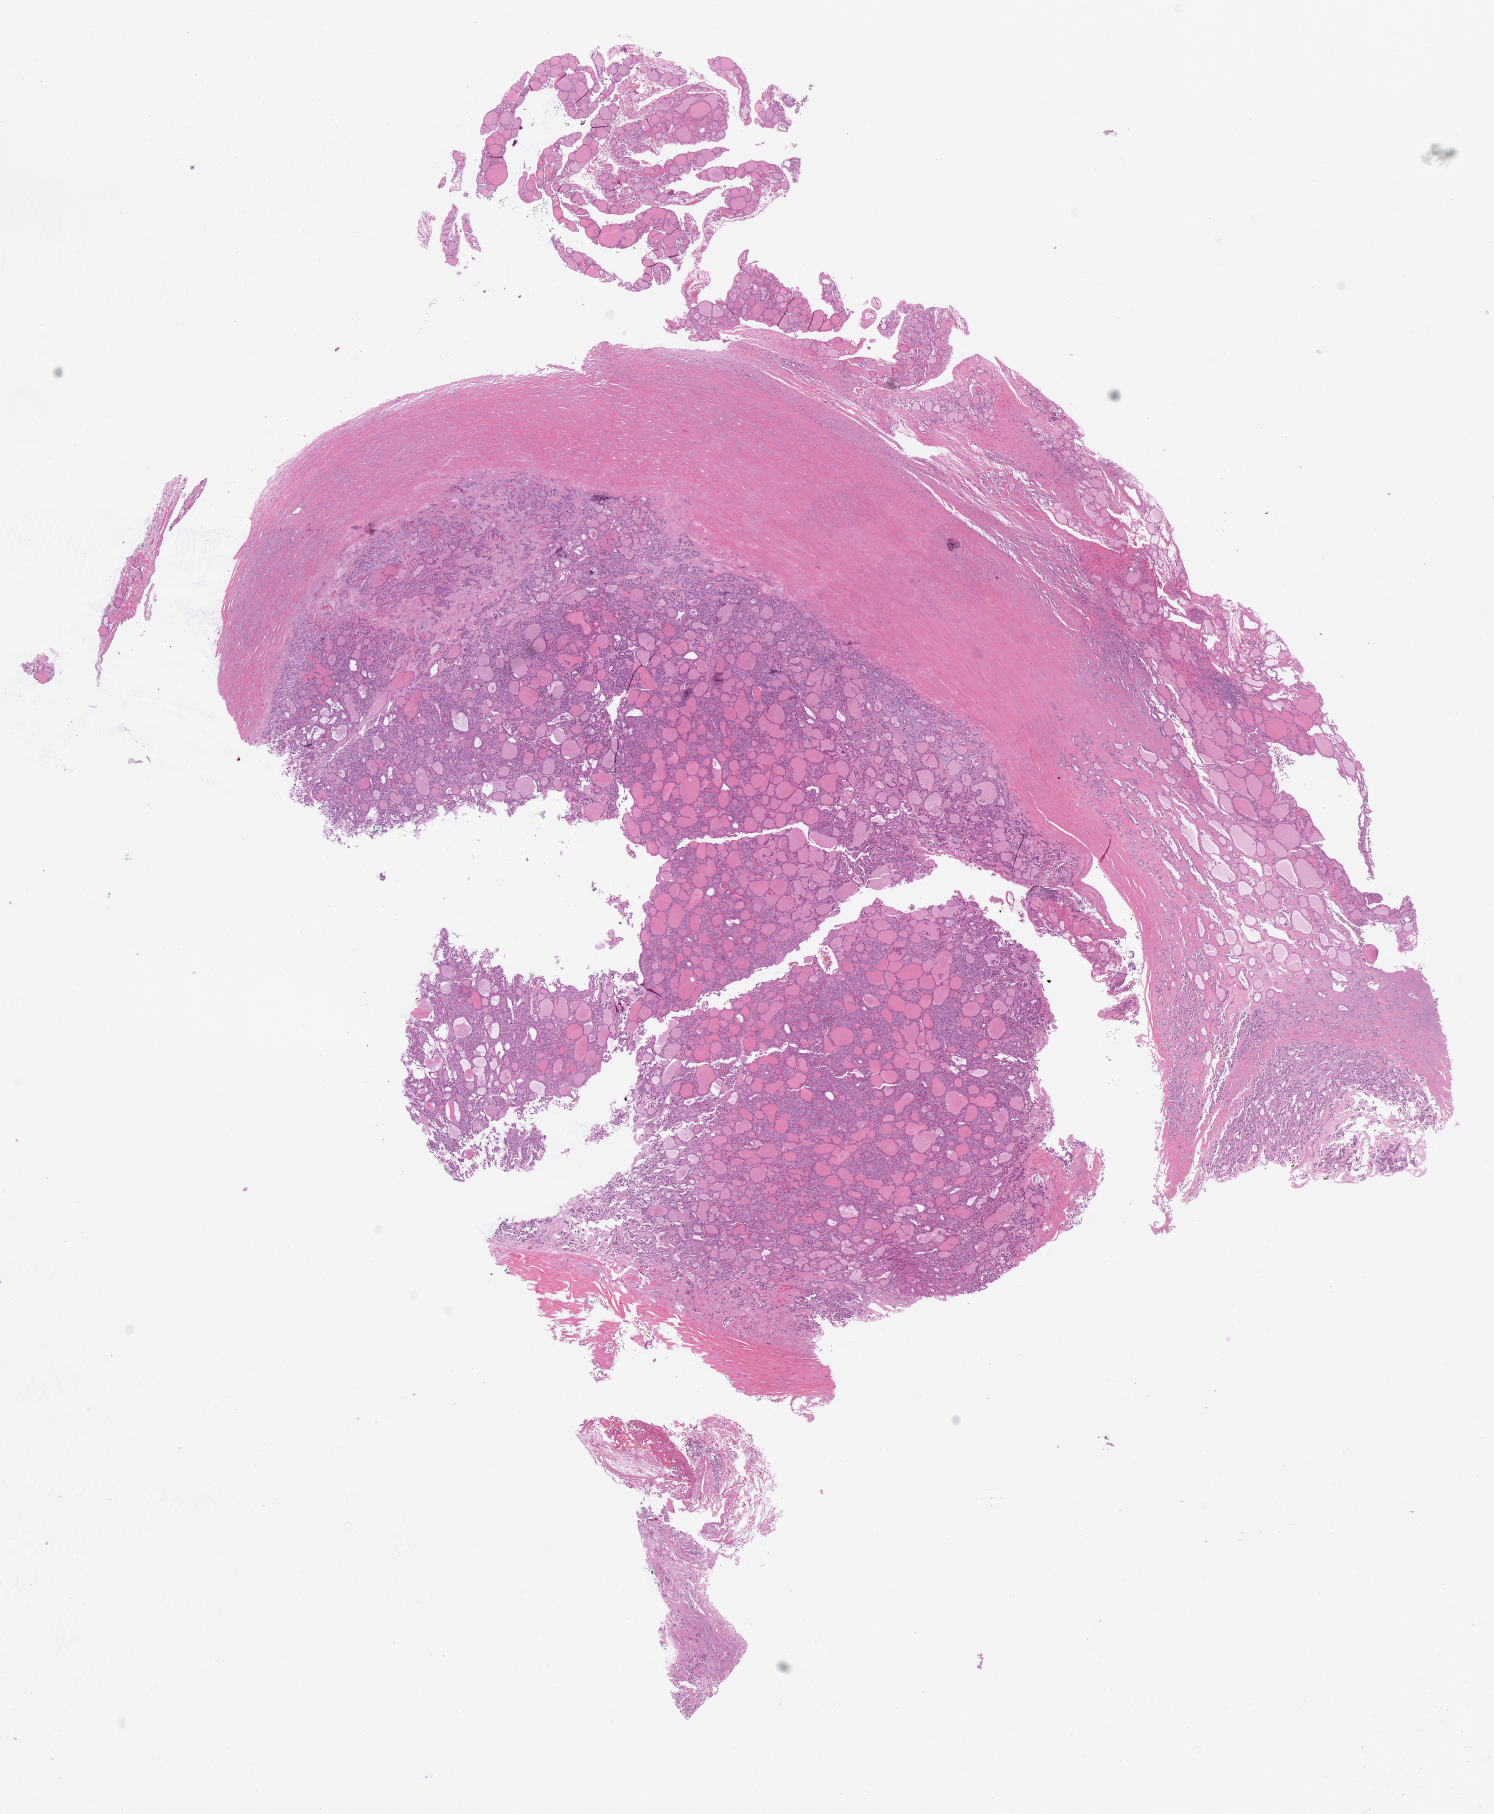
Whole-slide histology image, H&E-stained — low-resolution overview of the scanned area, about 11.7 x 14.3 mm (acquisition: 40x scan), formalin-fixed paraffin-embedded (FFPE) diagnostic section, primary tumour sample from the thyroid. Female patient; age at initial diagnosis 66 years.
Histologic diagnosis: Papillary carcinoma, follicular variant (thyroid gland). Lymph nodes positive (case pathology): 0 of 1 examined. AJCC pathologic stage: II (7th edition).